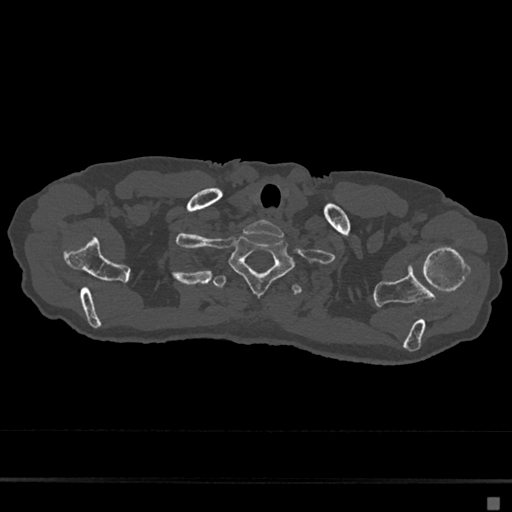
CT including the spine, one axial slice; reconstruction kernel Br40s/3; 120 kVp; bone window (W 1800 / L 400 HU); 0.5 mm slice thickness; 512 × 512 image matrix. Patient: female, 68 years. From the clinical record (not read from this slice): primary cancer: renal.
Outlined on this slice (semi-automatic segmentation, software-assisted and operator-edited):
- T1 vertebra: bounding box (x1, y1, x2, y2) in pixels: (229, 235, 294, 296)
- T2 vertebra: (213, 275, 303, 295)